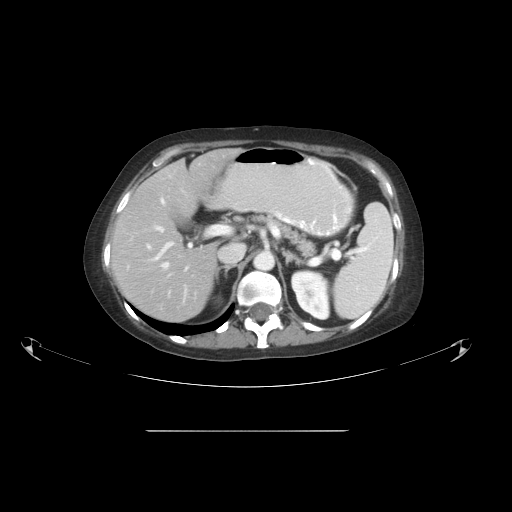
Contrast-enhanced abdominal CT, one axial slice; position 33 of 51 along the scan axis; reconstruction kernel STANDARD; intravenous contrast given; soft-tissue window (W 400 / L 40 HU); 512 × 512 image matrix, field of view 475 × 475 mm. Female patient, age 48 years. From the clinical record (not read from this slice): diagnosis: colorectal cancer liver metastases, imaged before liver resection; multiple liver metastases: yes; largest metastasis: 1 cm; disease in both lobes: no.
Structures marked on this image (manually delineated by an expert):
- hepatic veins: box from (x=145, y=199) to (x=224, y=286) px
- liver: (x=111, y=149)–(x=236, y=323)
- planned liver remnant (the part of the liver to remain after resection): (x=111, y=160)–(x=218, y=323)
- portal vein (with intrahepatic branches): (x=151, y=226)–(x=188, y=294)